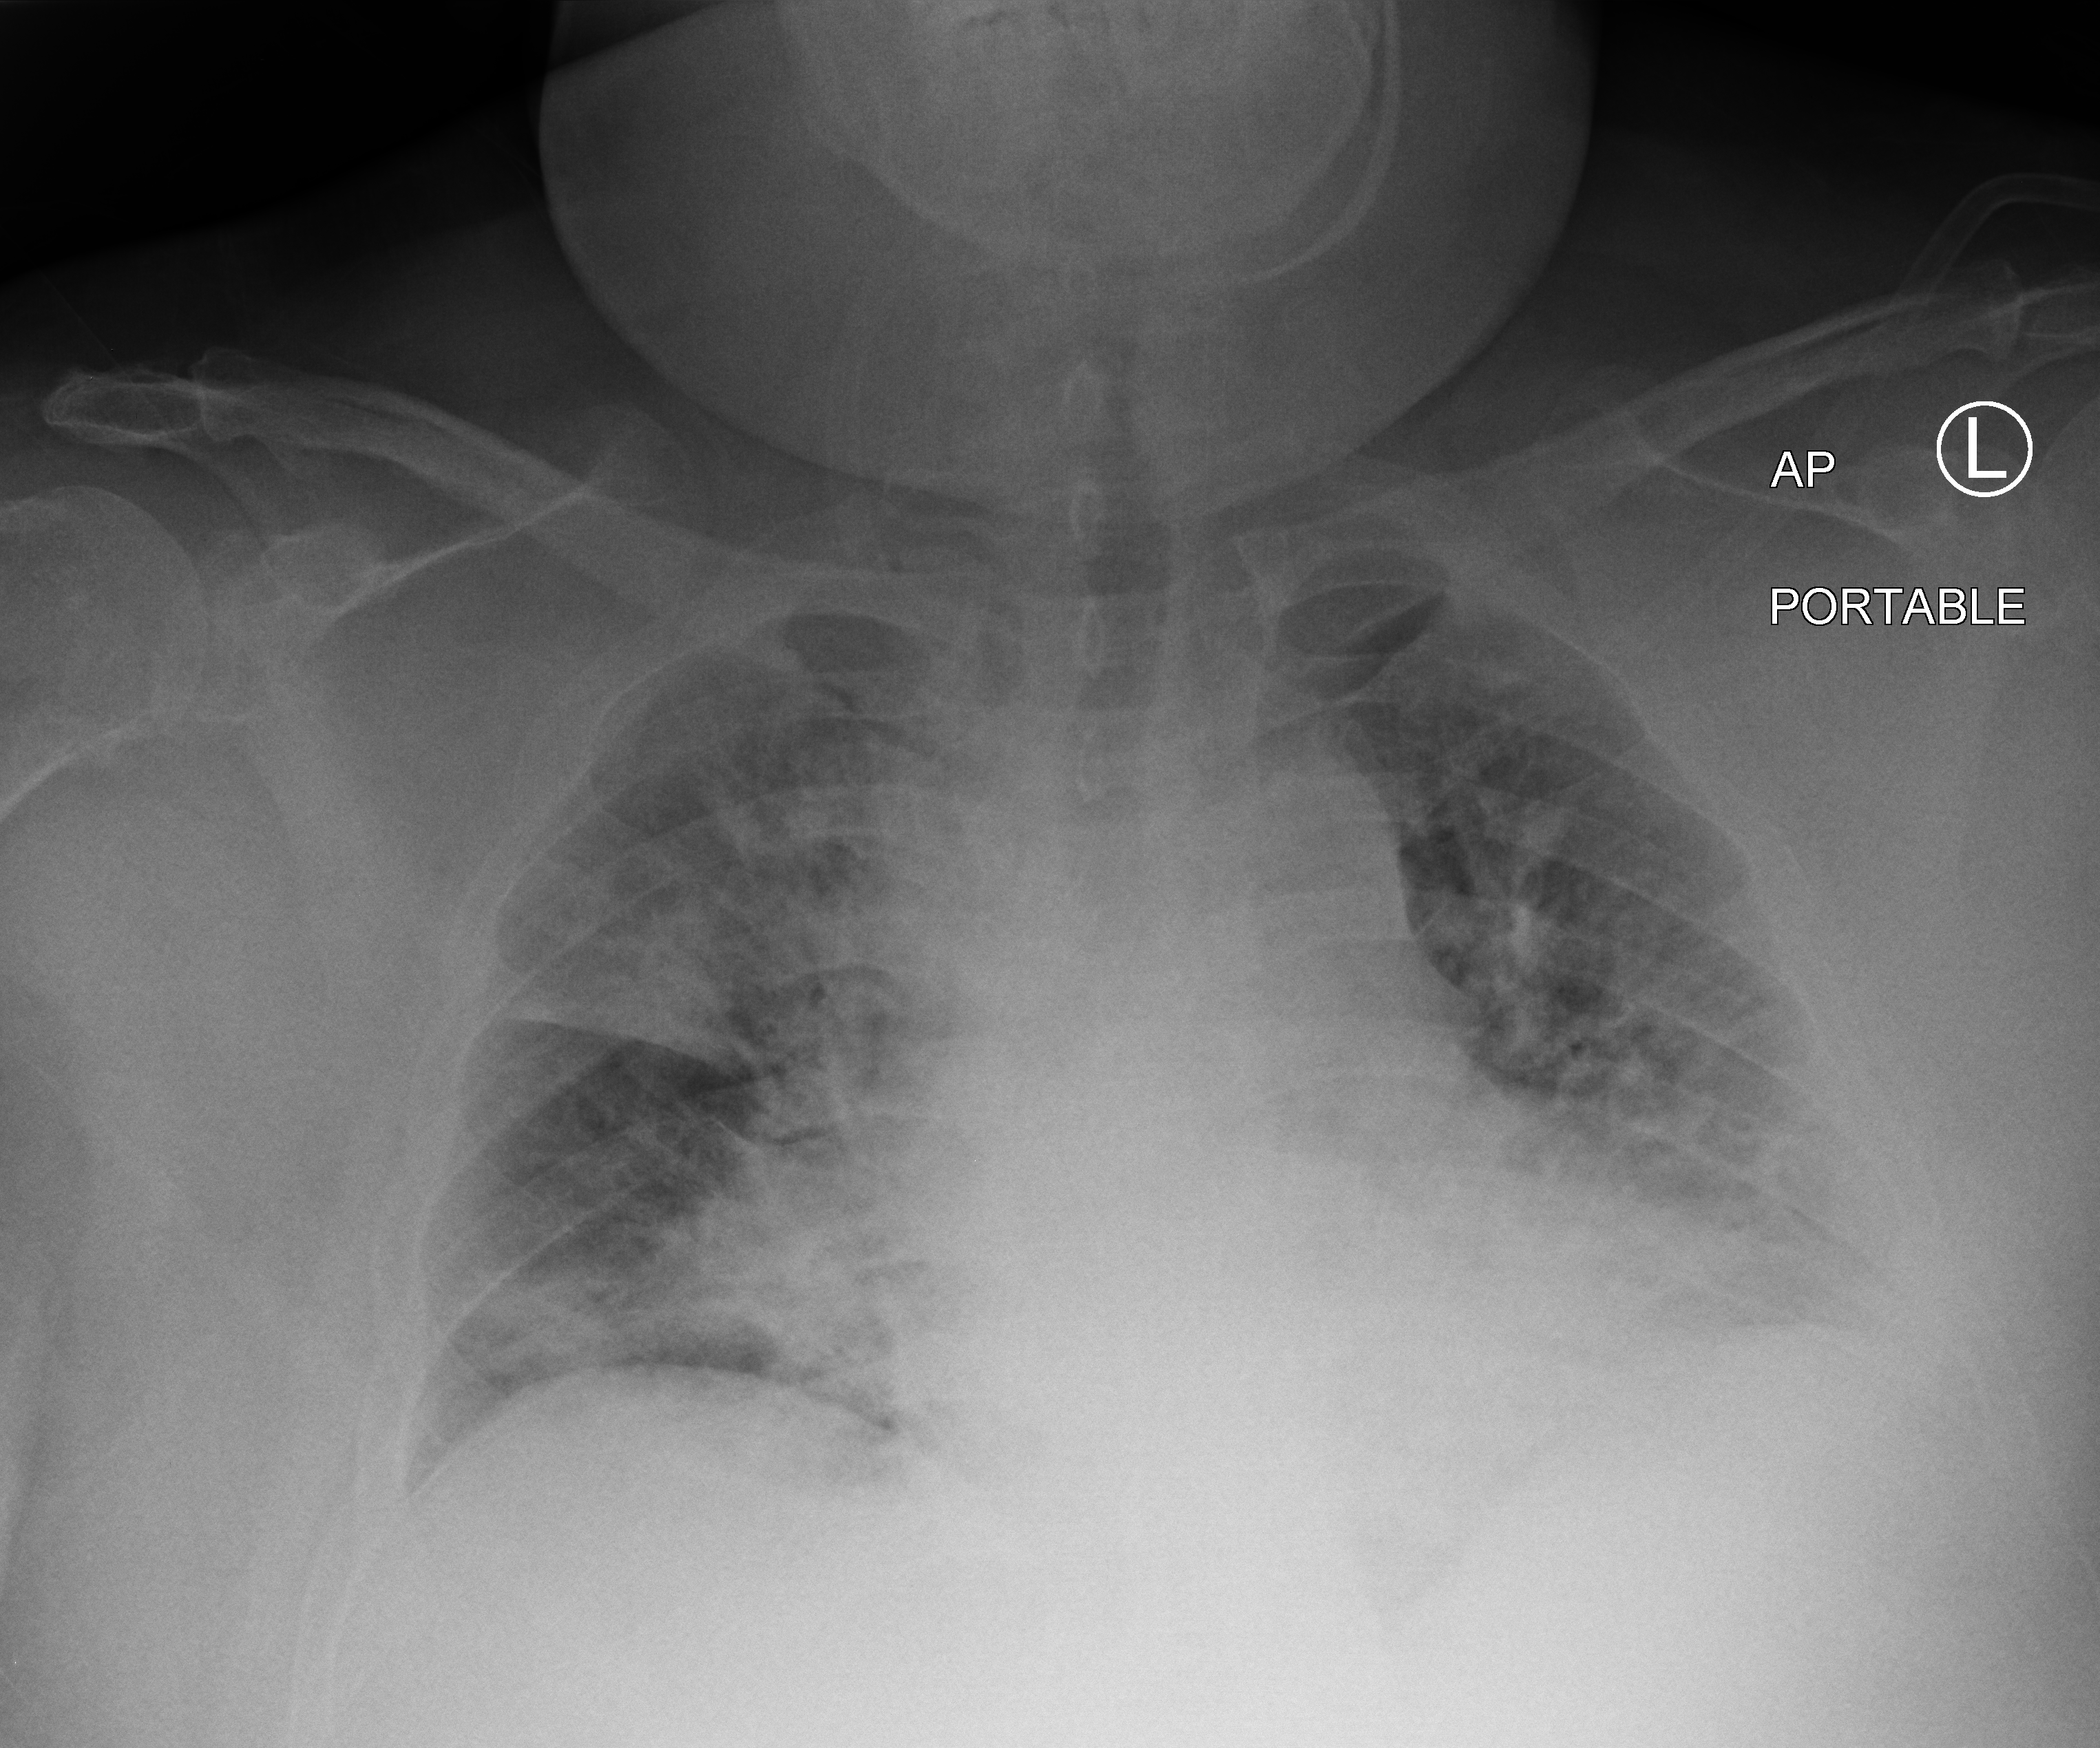
Chest X-ray (portable). Patient hospitalised with COVID-19; male, aged 18–59 years.
Hospital-stay facts (about this admission, not read from this image; timing relative to this image not recorded):
- COPD (admission record): no
- mechanically ventilated during this hospital stay: no